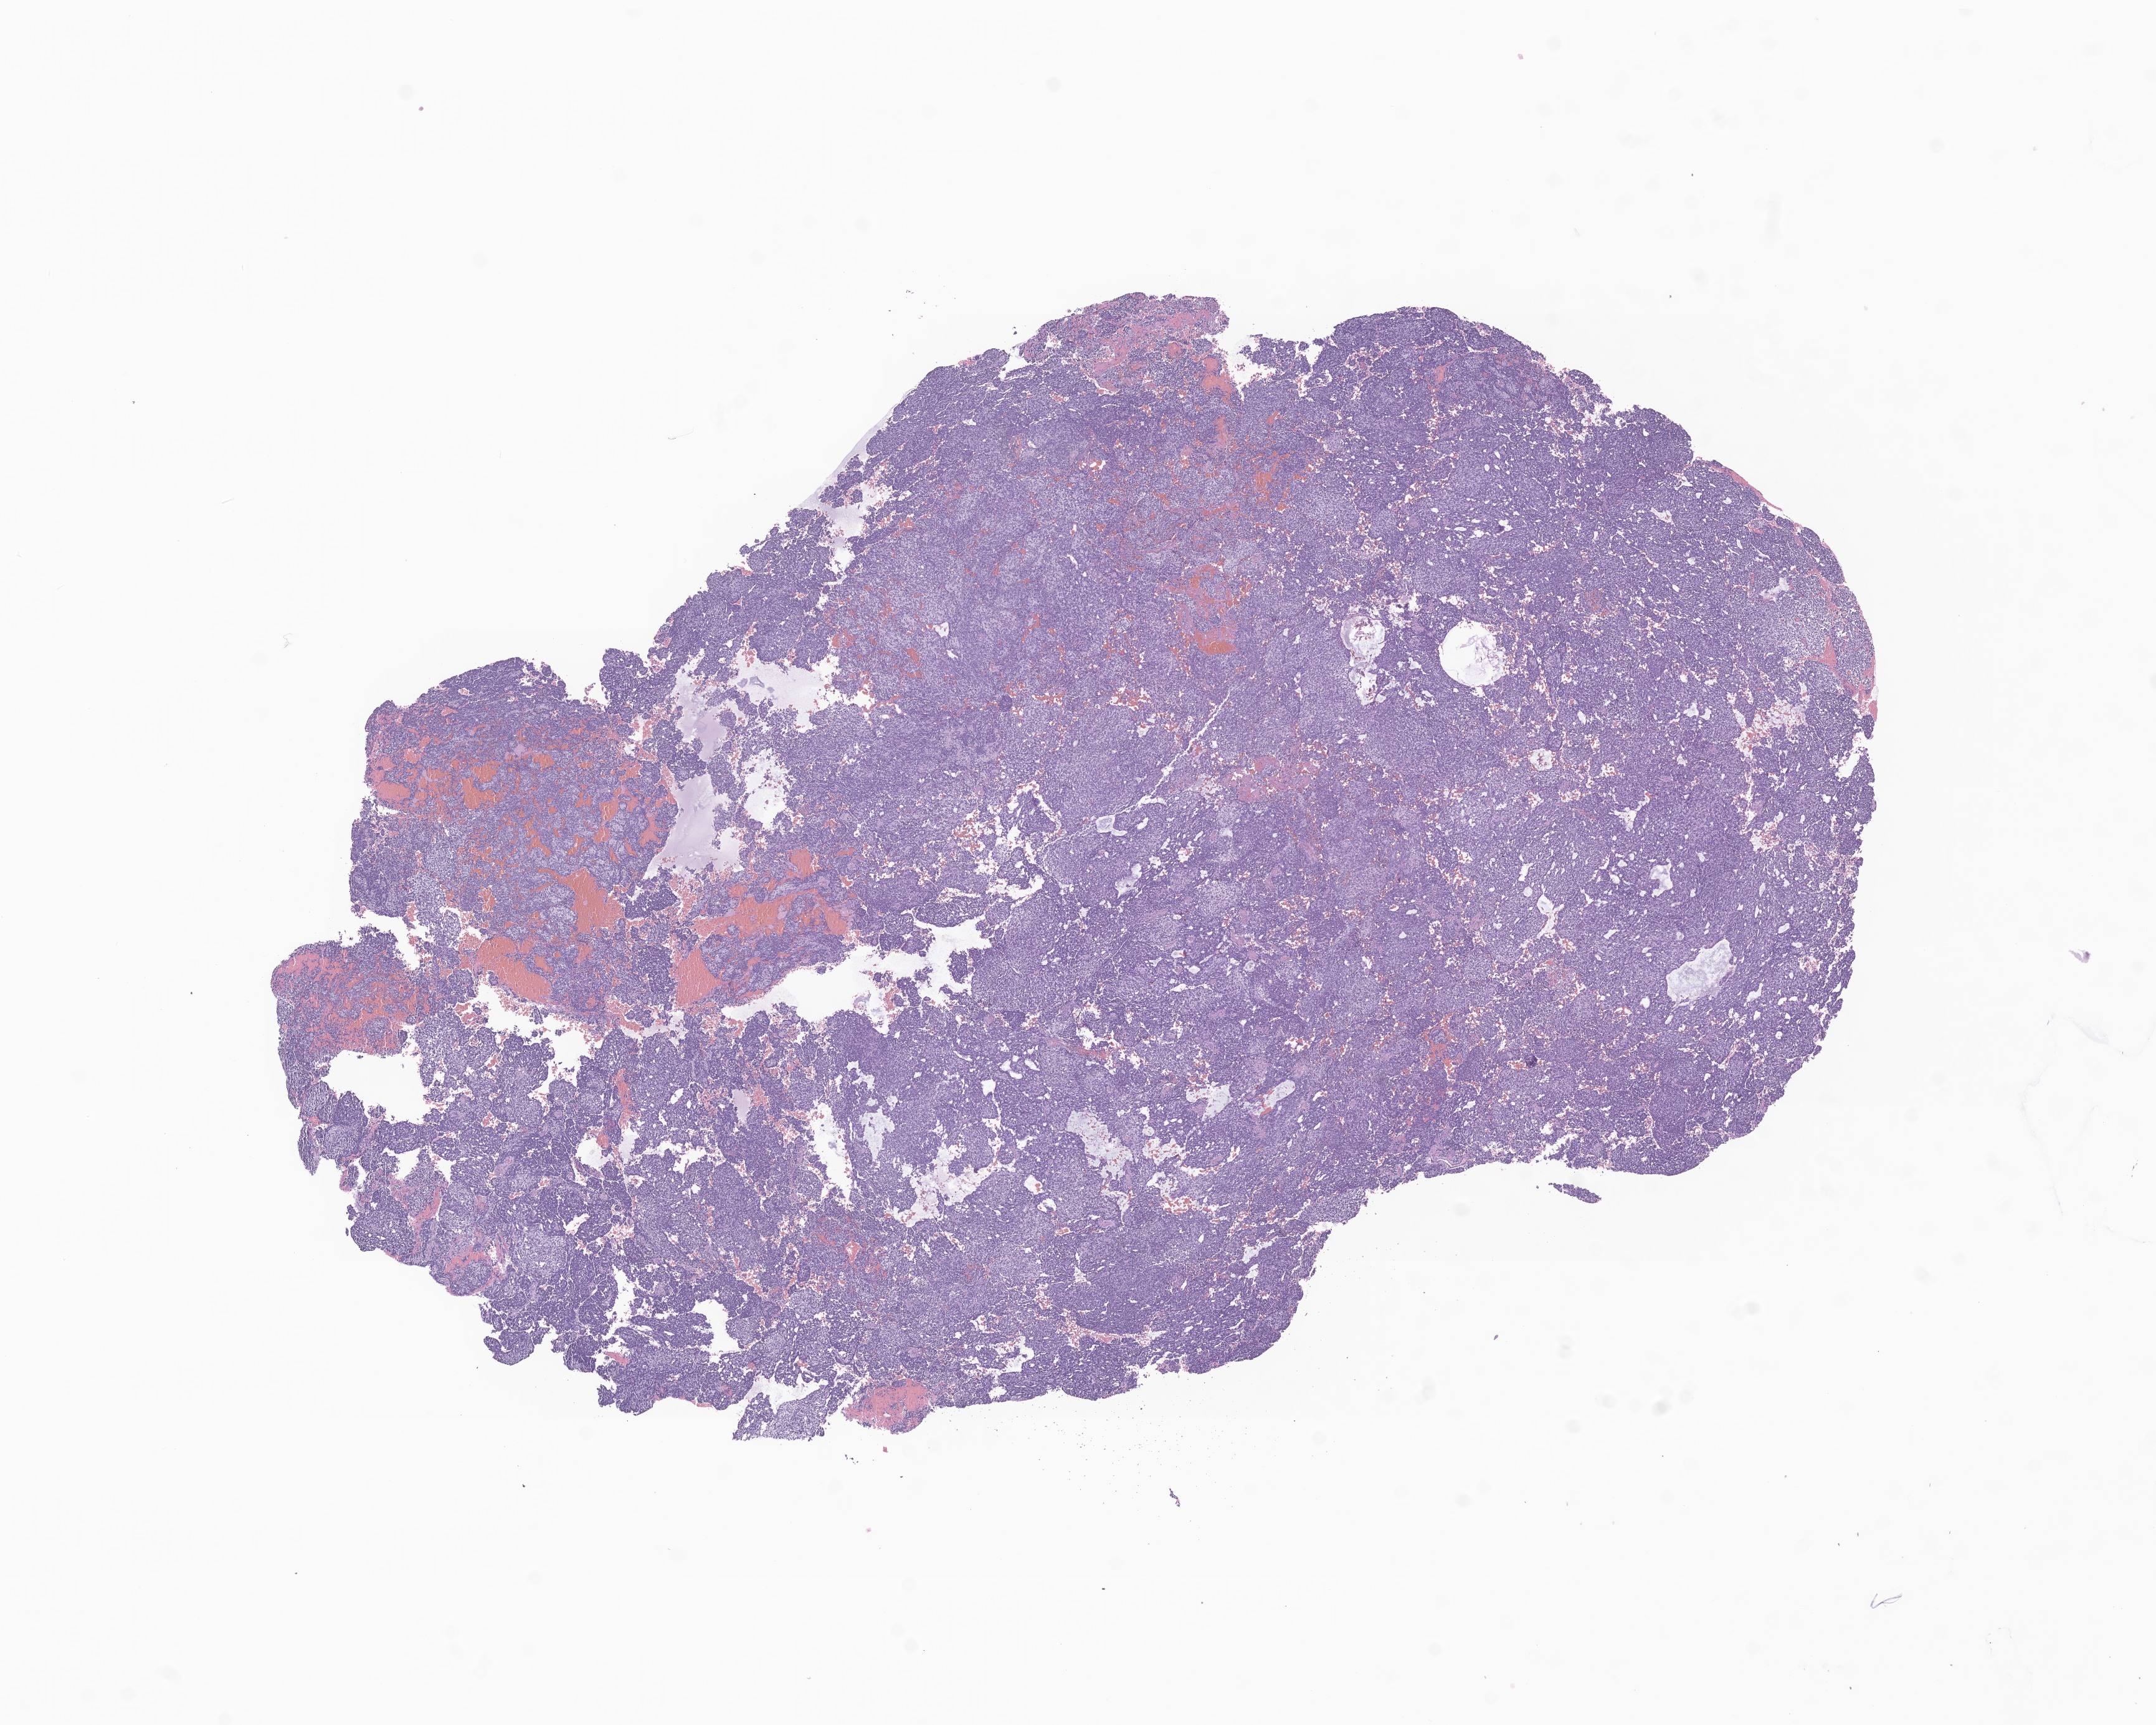
Whole-slide image, haematoxylin and eosin stain of tumor tissue from the brain, whole scanned area (about 14.6 x 11.7 mm) shown as a low-resolution overview. FFPE section. Patient: female, age 550 days (about 1.5 years).
• diagnosis: Medulloblastoma, NOS